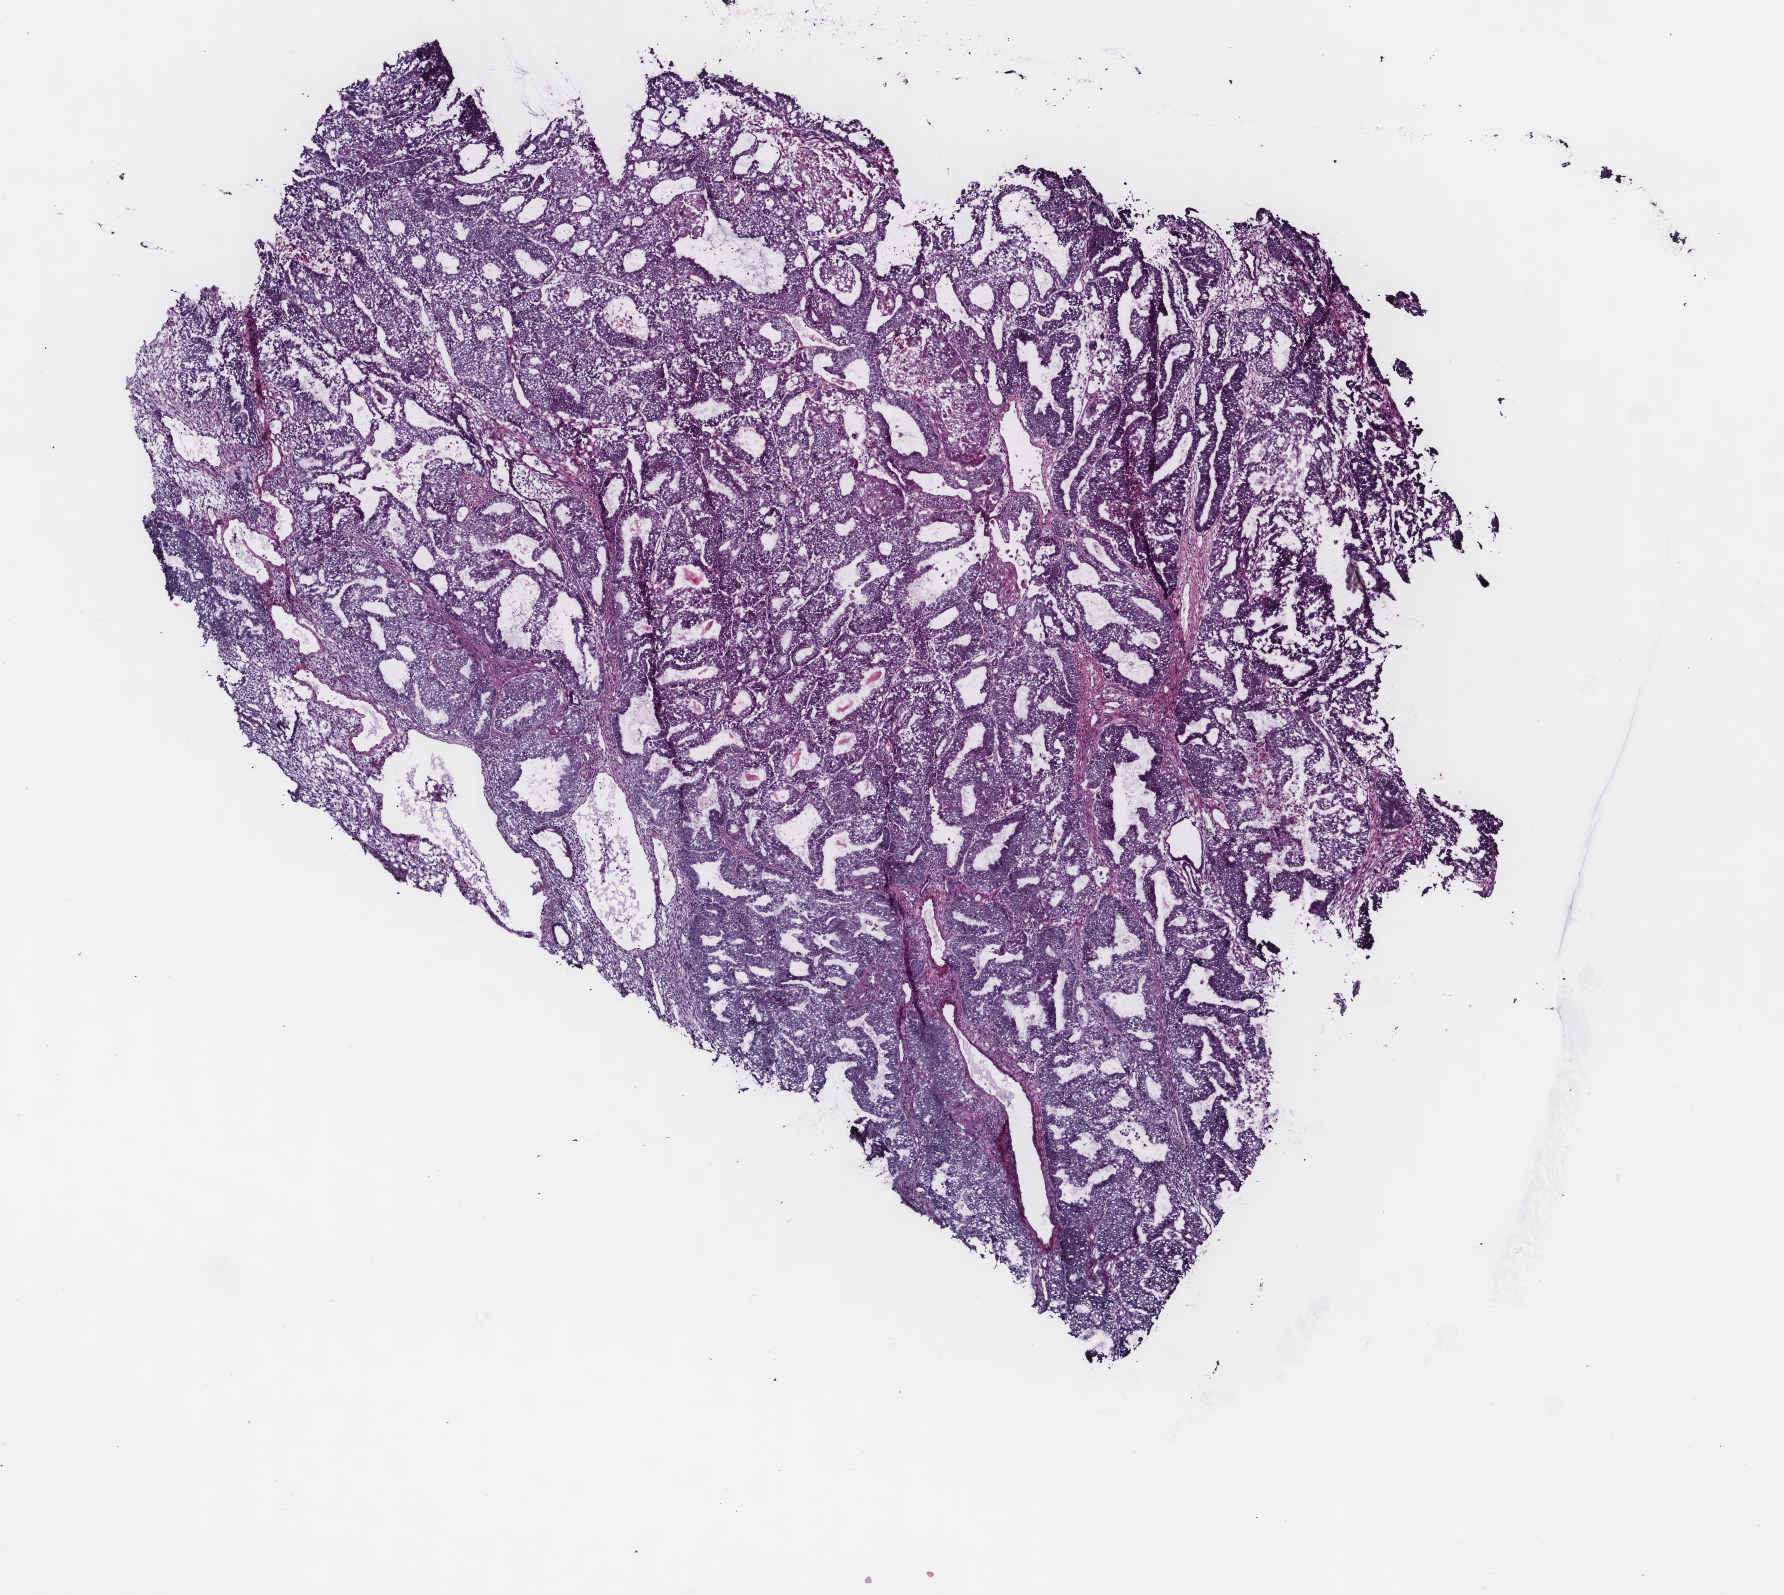
Digitized H&E tissue section (whole slide), a low-resolution overview of the entire scanned area, about 7.1 x 6.3 mm. Frozen section. Primary tumour sample from the uterus. Female patient; age at initial diagnosis 58 years. Histologic grade: G2 (moderately differentiated). Slide review estimates, as recorded: tumour cells 100%, tumour nuclei 80%, normal cells 0%, stromal cells 0%, necrosis 0%. Infiltration values recorded for this section: lymphocyte infiltration 0%, monocyte infiltration 0%, neutrophil infiltration 0%.
* pathologic diagnosis: Endometrioid adenocarcinoma, NOS (endometrium)
* FIGO stage: IA
* lymph nodes positive (case pathology): 0 of 11 examined